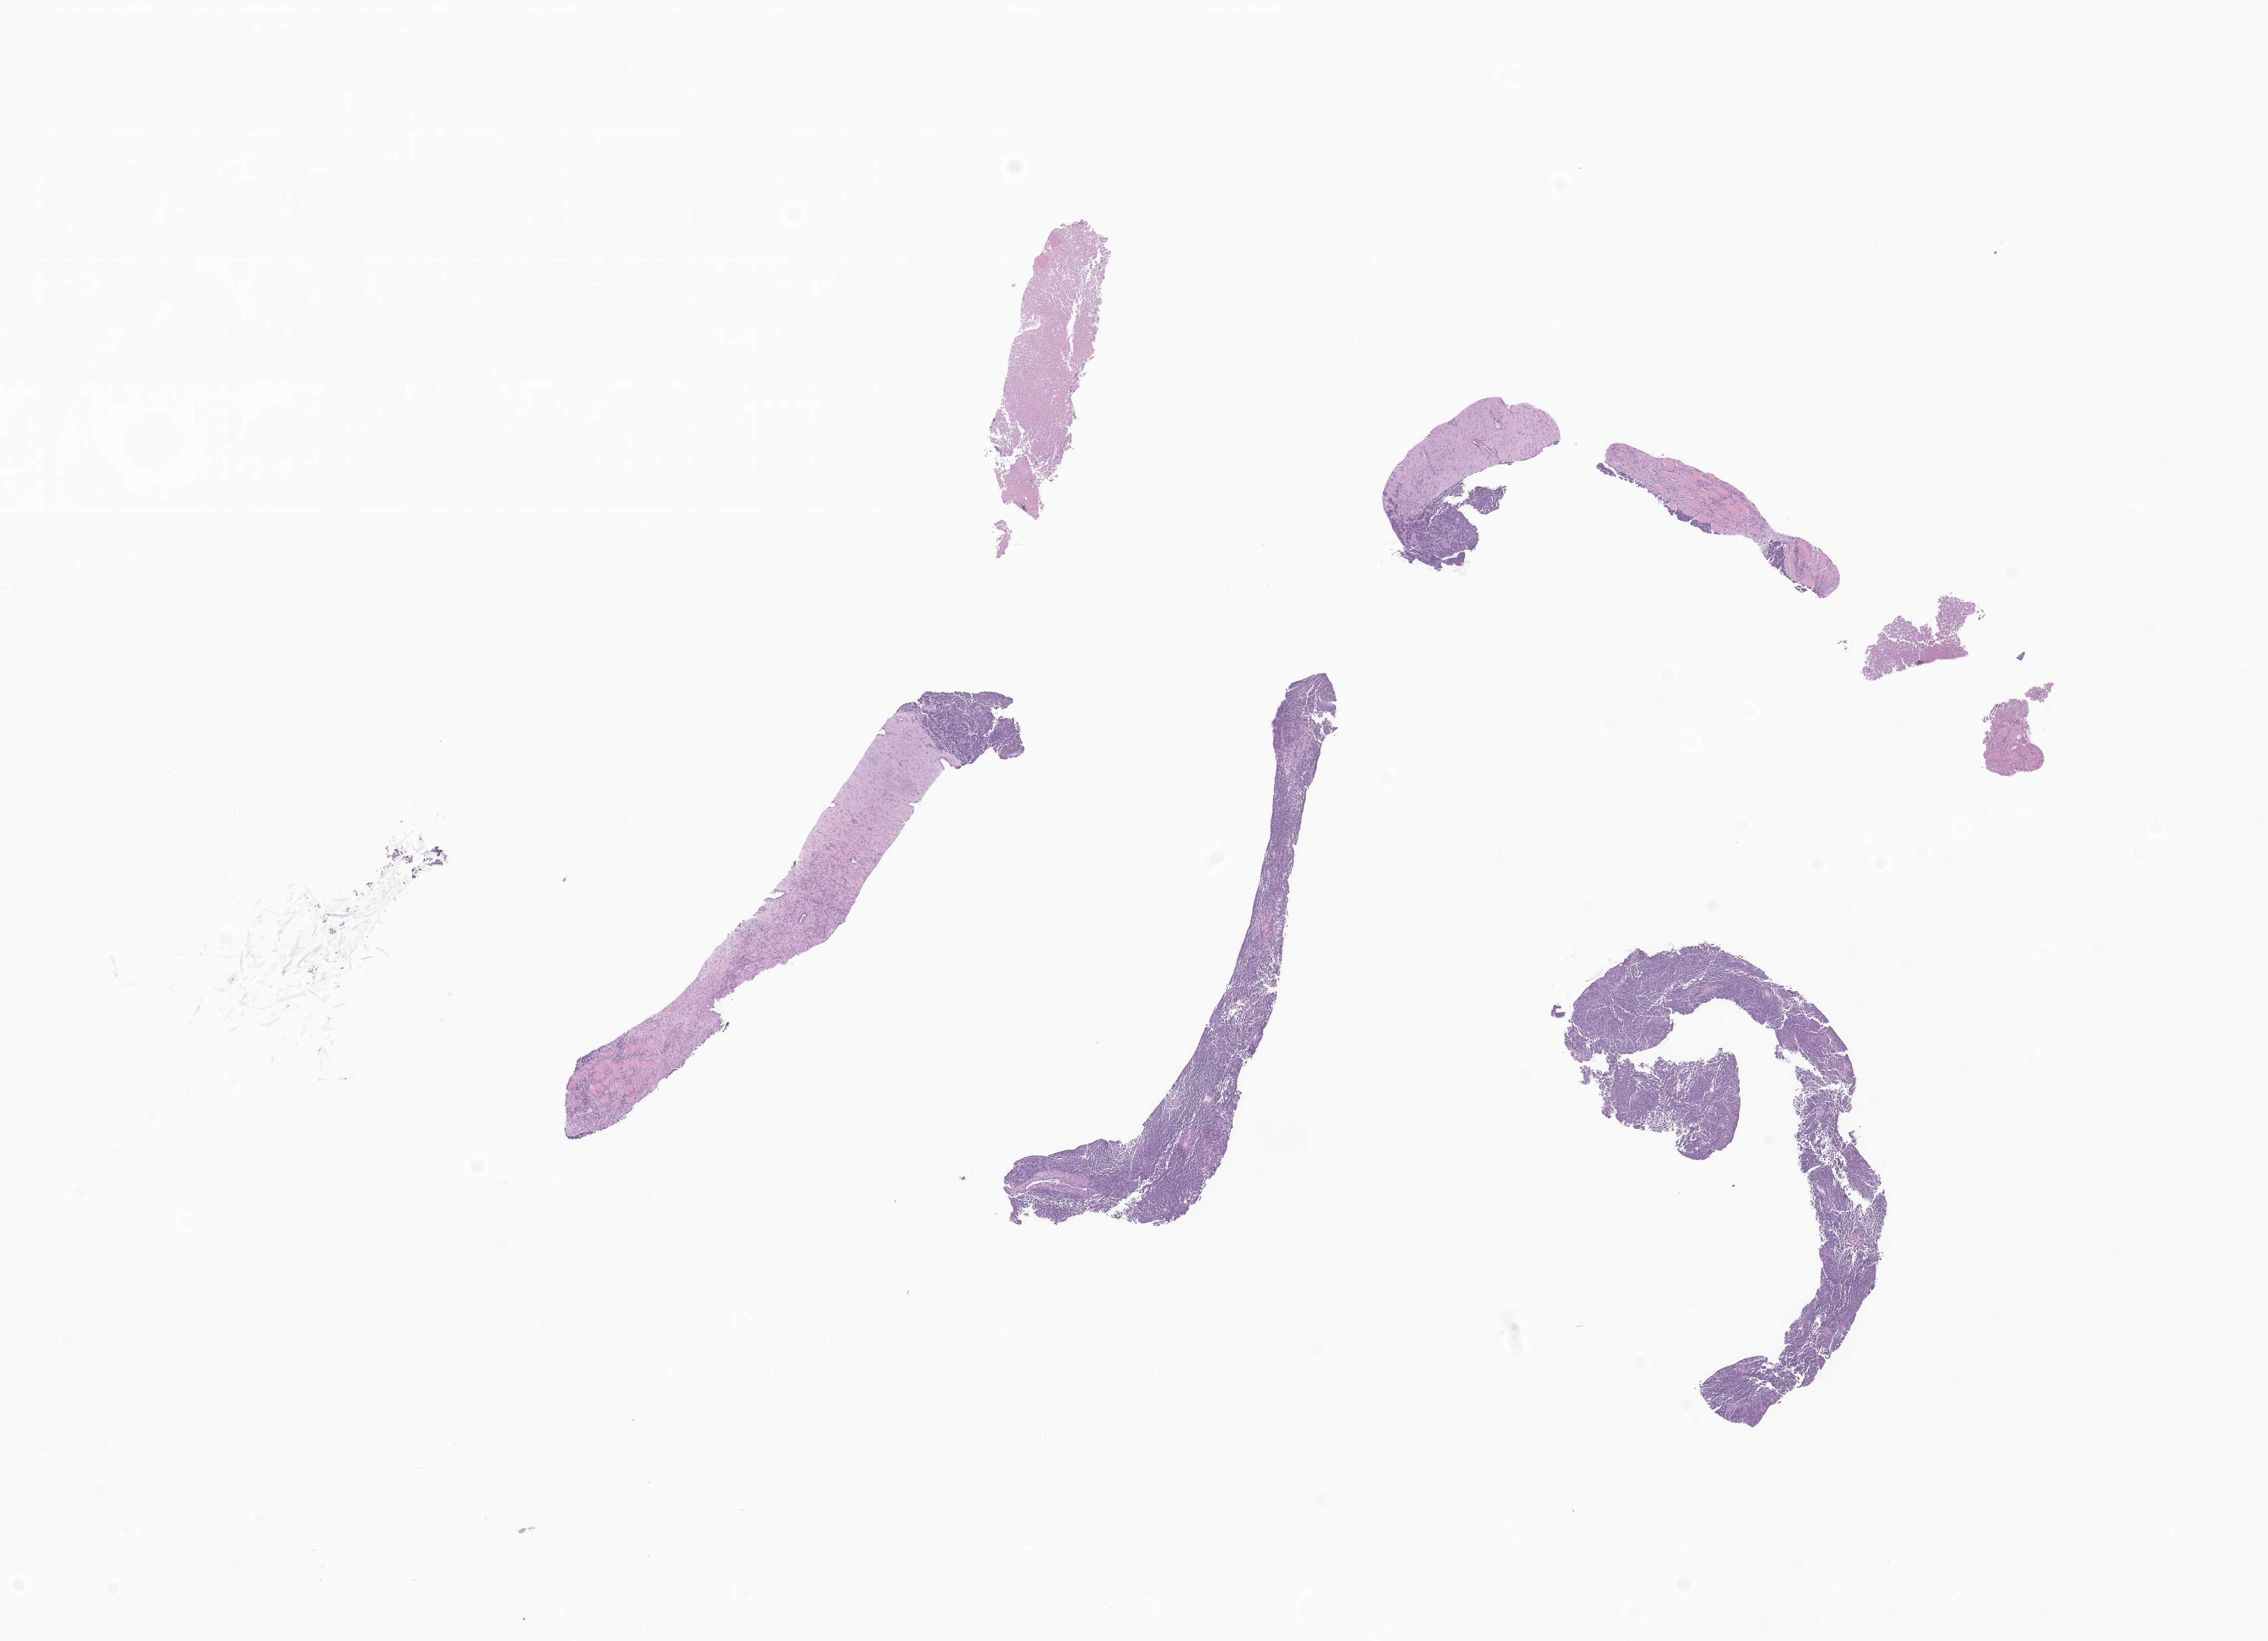
H&E whole-slide image of tumor tissue from the short bone of lower limb — whole scanned area (about 19.2 x 13.9 mm) shown as a low-resolution overview; FFPE section. Patient female; age 169 months.
Recorded diagnosis: Sarcoma, NOS.